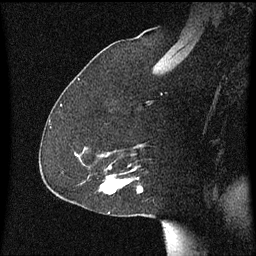
Breast MRI (dynamic contrast-enhanced), one sagittal slice; position 38 of 60 along the scan axis; dynamic contrast-enhanced series, image 2 of 3 at this slice position (ordered by acquisition); 1.5 T; TE 4.2 ms, TR 8.4 ms; 2 mm slice thickness; 256 × 256 image matrix. Female patient, age 59 years.
Structures marked on this image (semi-automatic segmentation, software-assisted and operator-edited):
- analysis volume of interest (the breast-tissue region the enhancement analysis was run in; not a lesion): bounding box (x1, y1, x2, y2) in pixels: (92, 166, 143, 195)
- tumour enhancement mask (voxels above the 70 % enhancement threshold inside the analysis volume of interest): (104, 176, 129, 189)